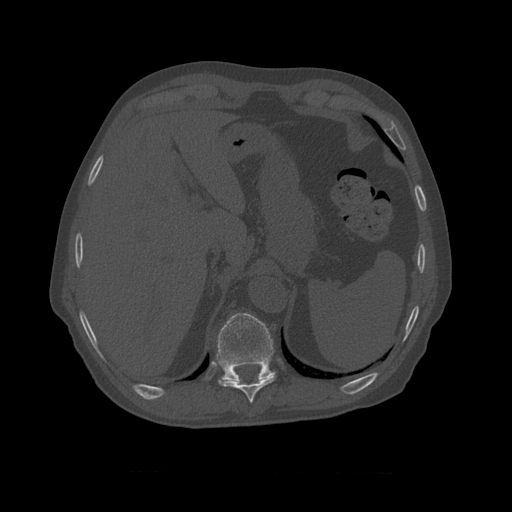
CT including the spine, one axial slice; slice 413 of 450 in the series (ordered by position); reconstruction kernel STANDARD; bone window (W 1800 / L 400 HU); 512 × 512 image matrix, field of view 405 × 405 mm. Patient age 75 years. Case-level facts recorded for this patient, not image findings: primary cancer: prostate.
Outlined on this slice (semi-automatic segmentation, software-assisted and operator-edited):
- T10 vertebra: box from (x=216, y=313) to (x=276, y=382) px
- T9 vertebra: (x=218, y=374)–(x=276, y=404)